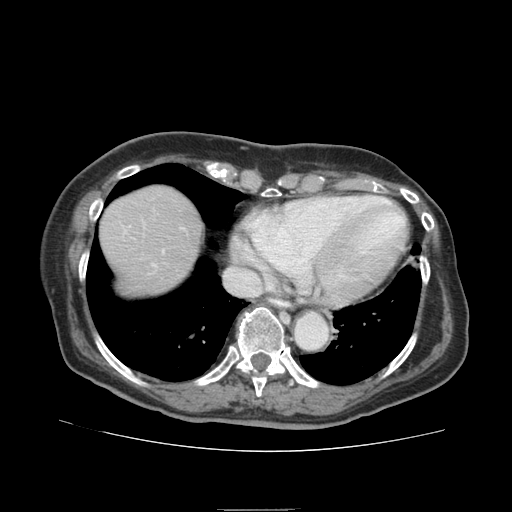
Contrast-enhanced abdominal CT (liver protocol), one axial slice. Position 75 of 95 along the scan axis. Reconstruction kernel STANDARD. 140 kVp. Soft-tissue window (W 400 / L 40 HU). 2.5 mm slice thickness. 512 × 512 image matrix, field of view 360 × 360 mm. Case-level facts recorded for this patient, not image findings: diagnosis: hepatocellular carcinoma (patient treated with transarterial chemoembolisation; whether this scan precedes or follows treatment is not stated here); TNM stage (as recorded): Stage-IVA; Child-Pugh class: B; tumour nodularity: uninodular.
Annotated regions visible in this slice (semi-automatic segmentation, software-assisted and operator-edited):
- abdominal aorta: bounding box (x1, y1, x2, y2) in pixels: (295, 312, 327, 349)
- liver parenchyma outside the tumour (the mass and vessels are separate outlines, so this box may not span the whole liver): (100, 186, 202, 294)